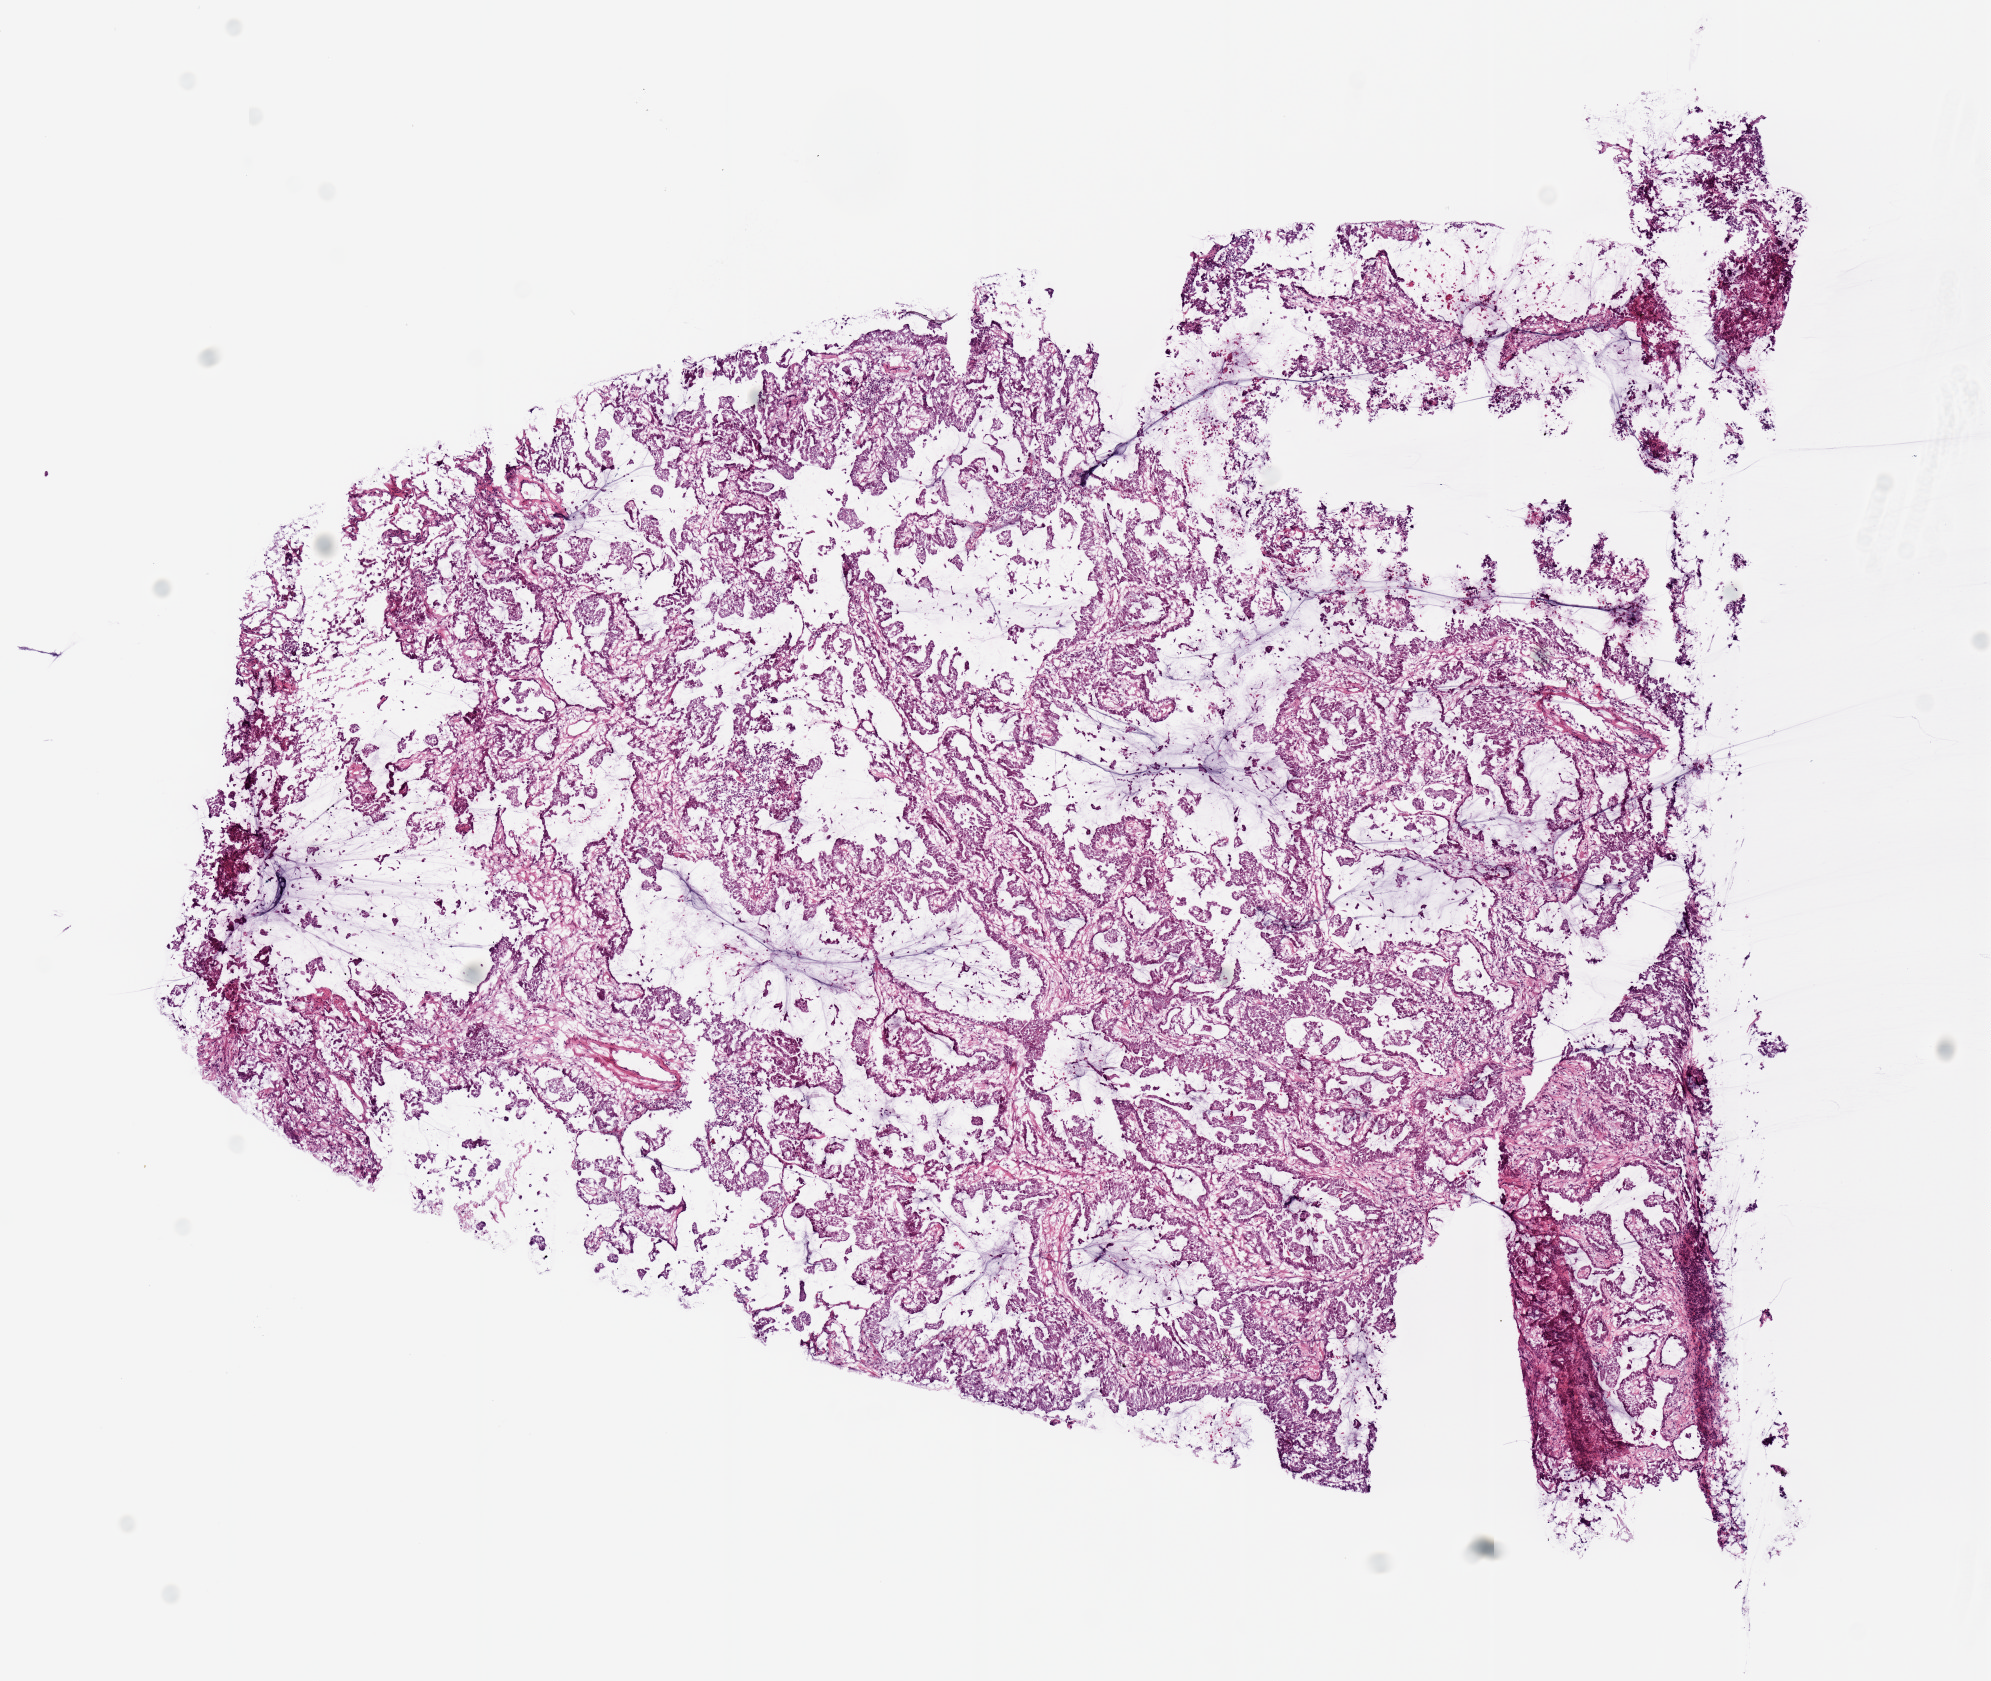
H&E-stained whole-slide image, whole scanned area (about 7.9 x 6.6 mm) shown as a low-resolution overview; frozen section from the top of the tissue portion; sample: primary tumour, lung. Female patient; age at initial diagnosis 67 years. Composition of this section per pathologist review: tumour cells 100%, tumour nuclei 80%, normal cells 0%, stromal cells 0%, necrosis 0%. Inflammatory infiltration, as recorded: lymphocyte infiltration 2%, monocyte infiltration 5%, neutrophil infiltration 0%.
Pathologic diagnosis: Papillary adenocarcinoma, NOS (upper lobe, lung). AJCC pathologic stage: IIIA (6th edition).